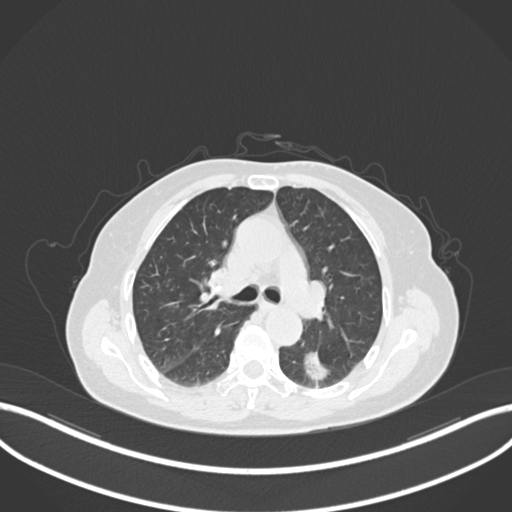
Chest CT, one axial slice; position 536 of 727 along the scan axis; reconstruction kernel B30f; lung window (W 1500 / L -600 HU); 1 mm slice thickness; 512 × 512 image matrix, field of view 400 × 400 mm. Patient: female, 70 years. From the clinical record (not read from this slice): clinical TNM (as recorded): T1c N0 M0.
Outlined on this slice (rectangle marked by the reading radiologist):
- lung tumour (recorded histology: adenocarcinoma): bounding box <299,347,337,384> (left, top, right, bottom; pixels)